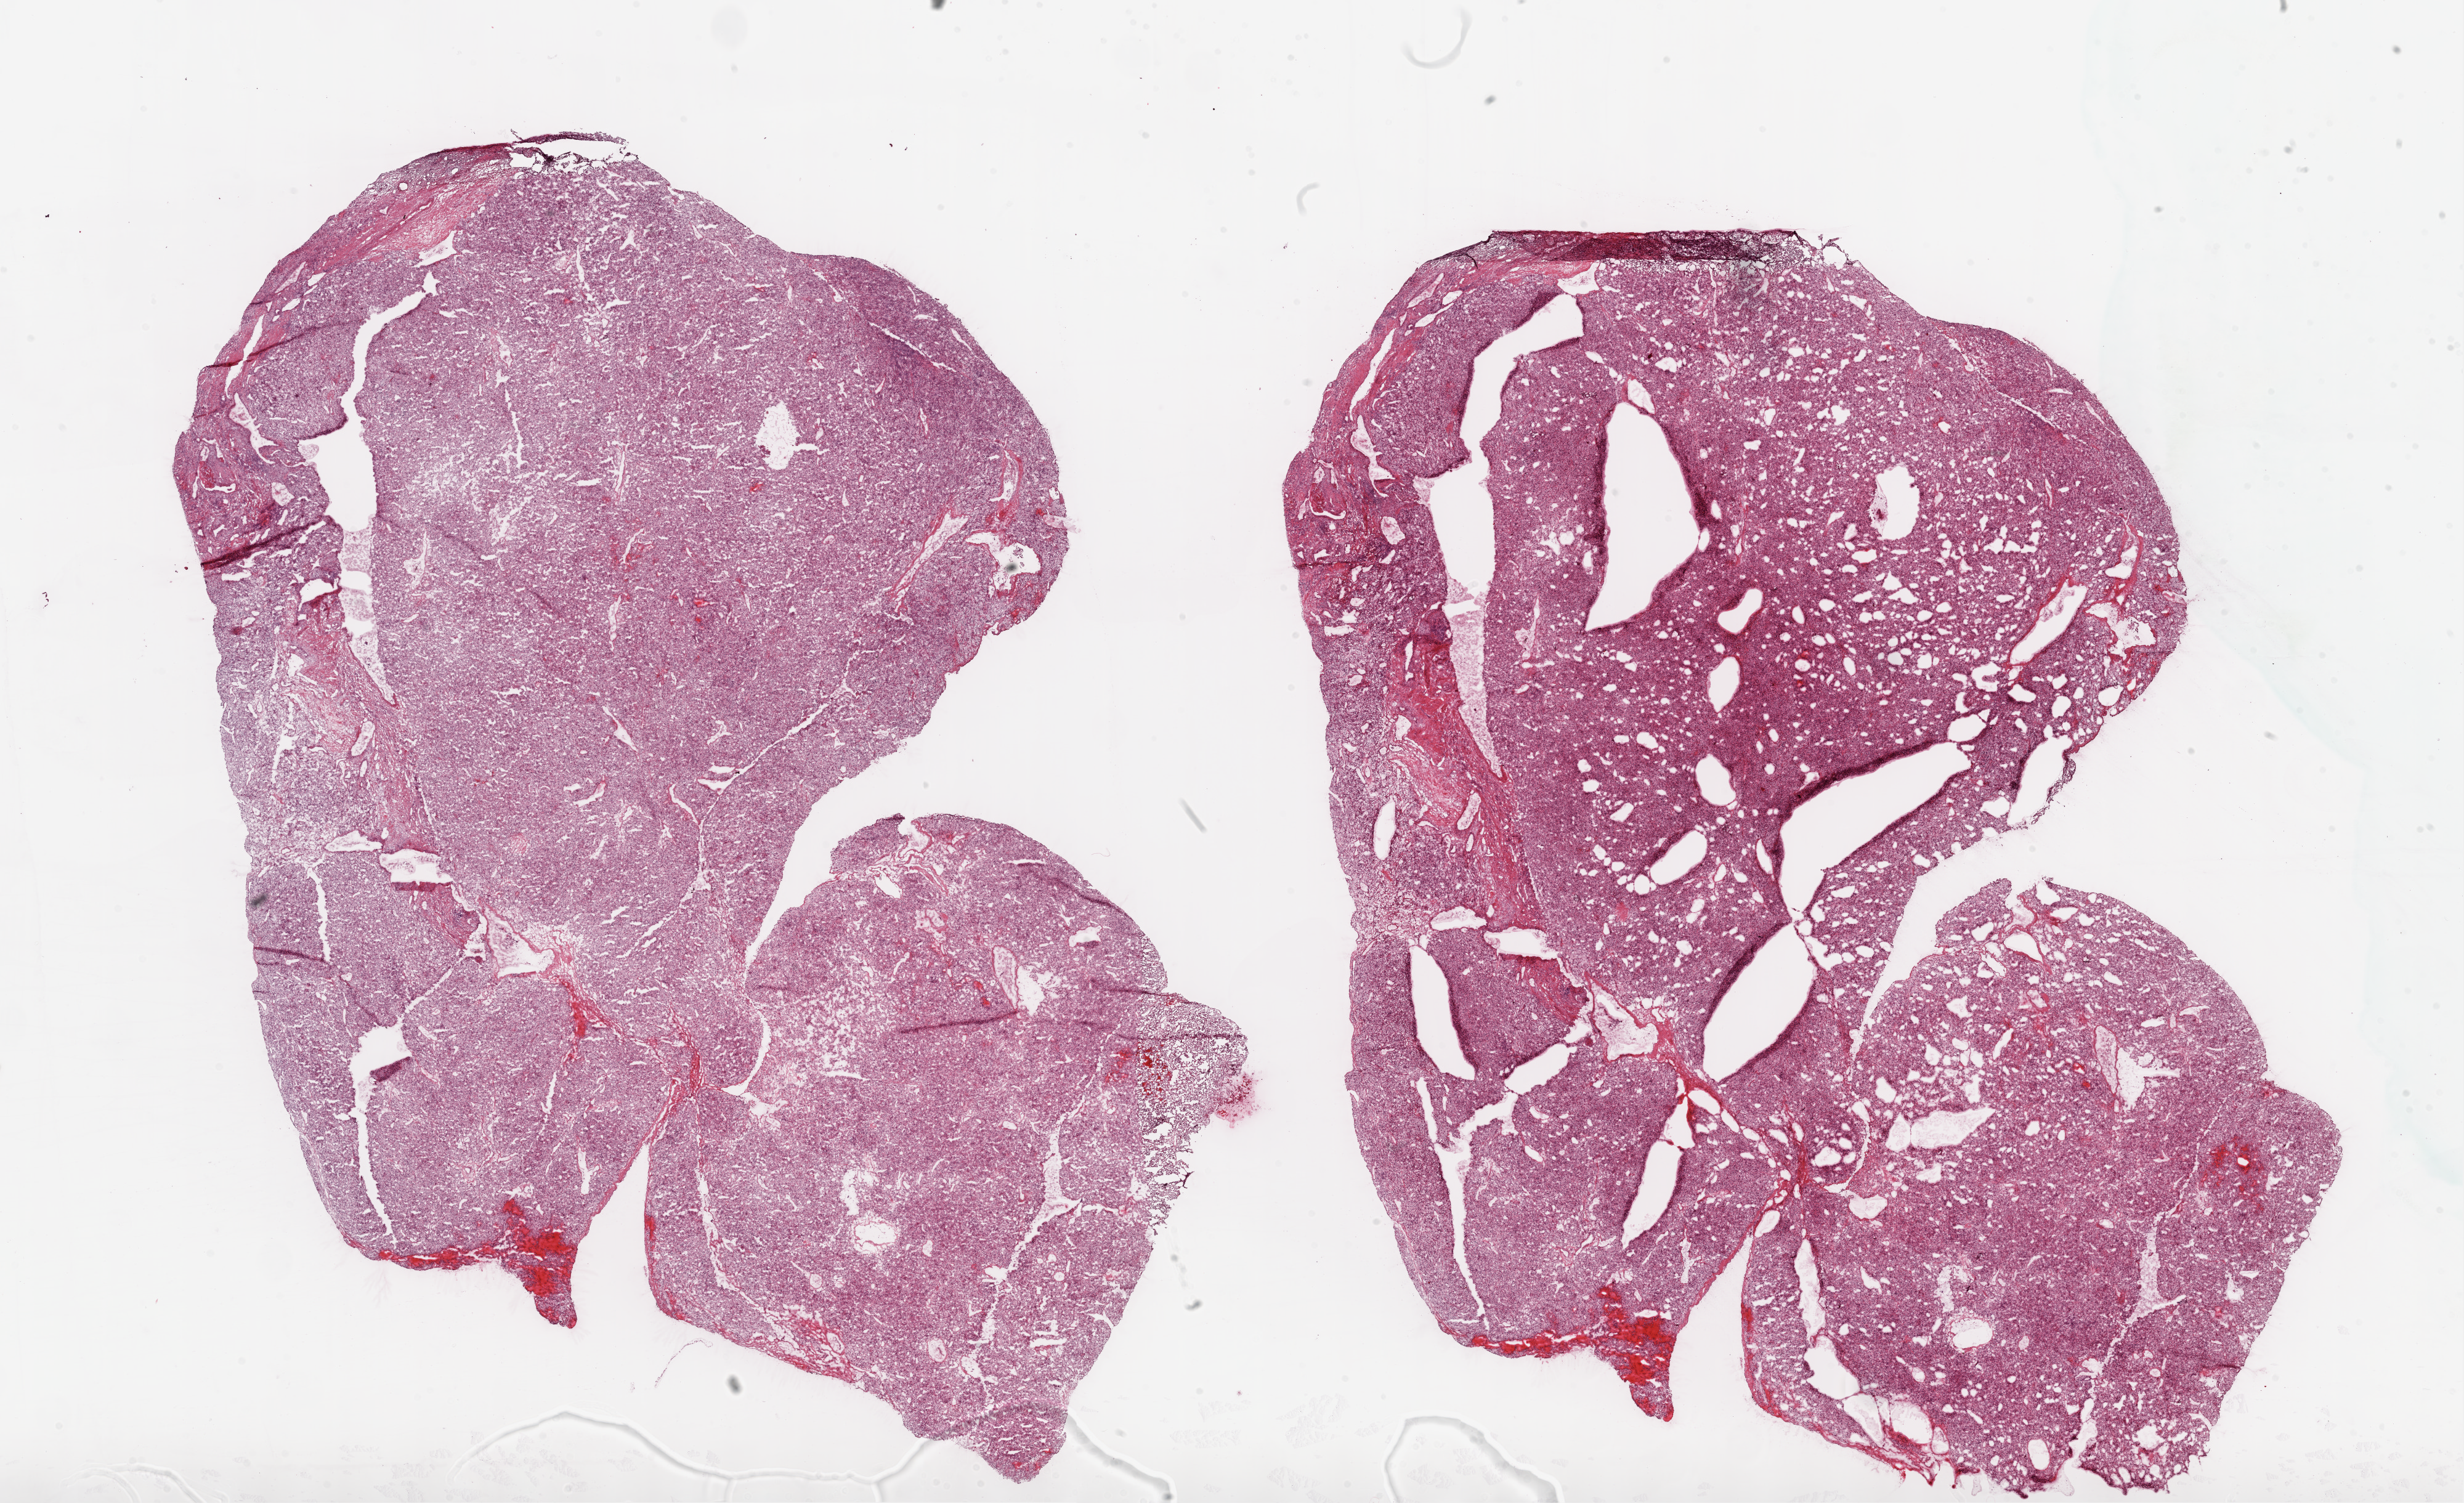
Whole-slide histology image, H&E — whole scanned area (about 32.1 x 19.6 mm, slide scanned at 20x) shown as a low-resolution overview; frozen section; kidney, primary tumour sample. Male, age 40 years at initial diagnosis. Histologic grade: G2 (moderately differentiated). Slide review estimates, as recorded: tumour cells 95%, tumour nuclei 95%, necrosis 5%. Inflammatory infiltration, as recorded: lymphocyte infiltration 1%.
- pathologic diagnosis: Clear cell adenocarcinoma, NOS
- AJCC pathologic stage: I